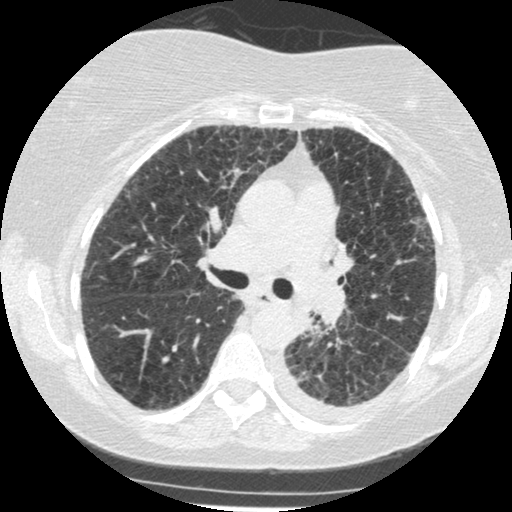
Low-dose screening chest CT, one axial slice. Slice 166 of 341 in the series (ordered by position). 120 kVp. Lung window (W 1500 / L -600 HU). 1.25 mm slice thickness. 512 × 512 image matrix.
Annotated regions visible in this slice (manually delineated by an expert):
- lesion 1 (tumor, lower lobe of left lung): box from (x=296, y=309) to (x=312, y=333) px